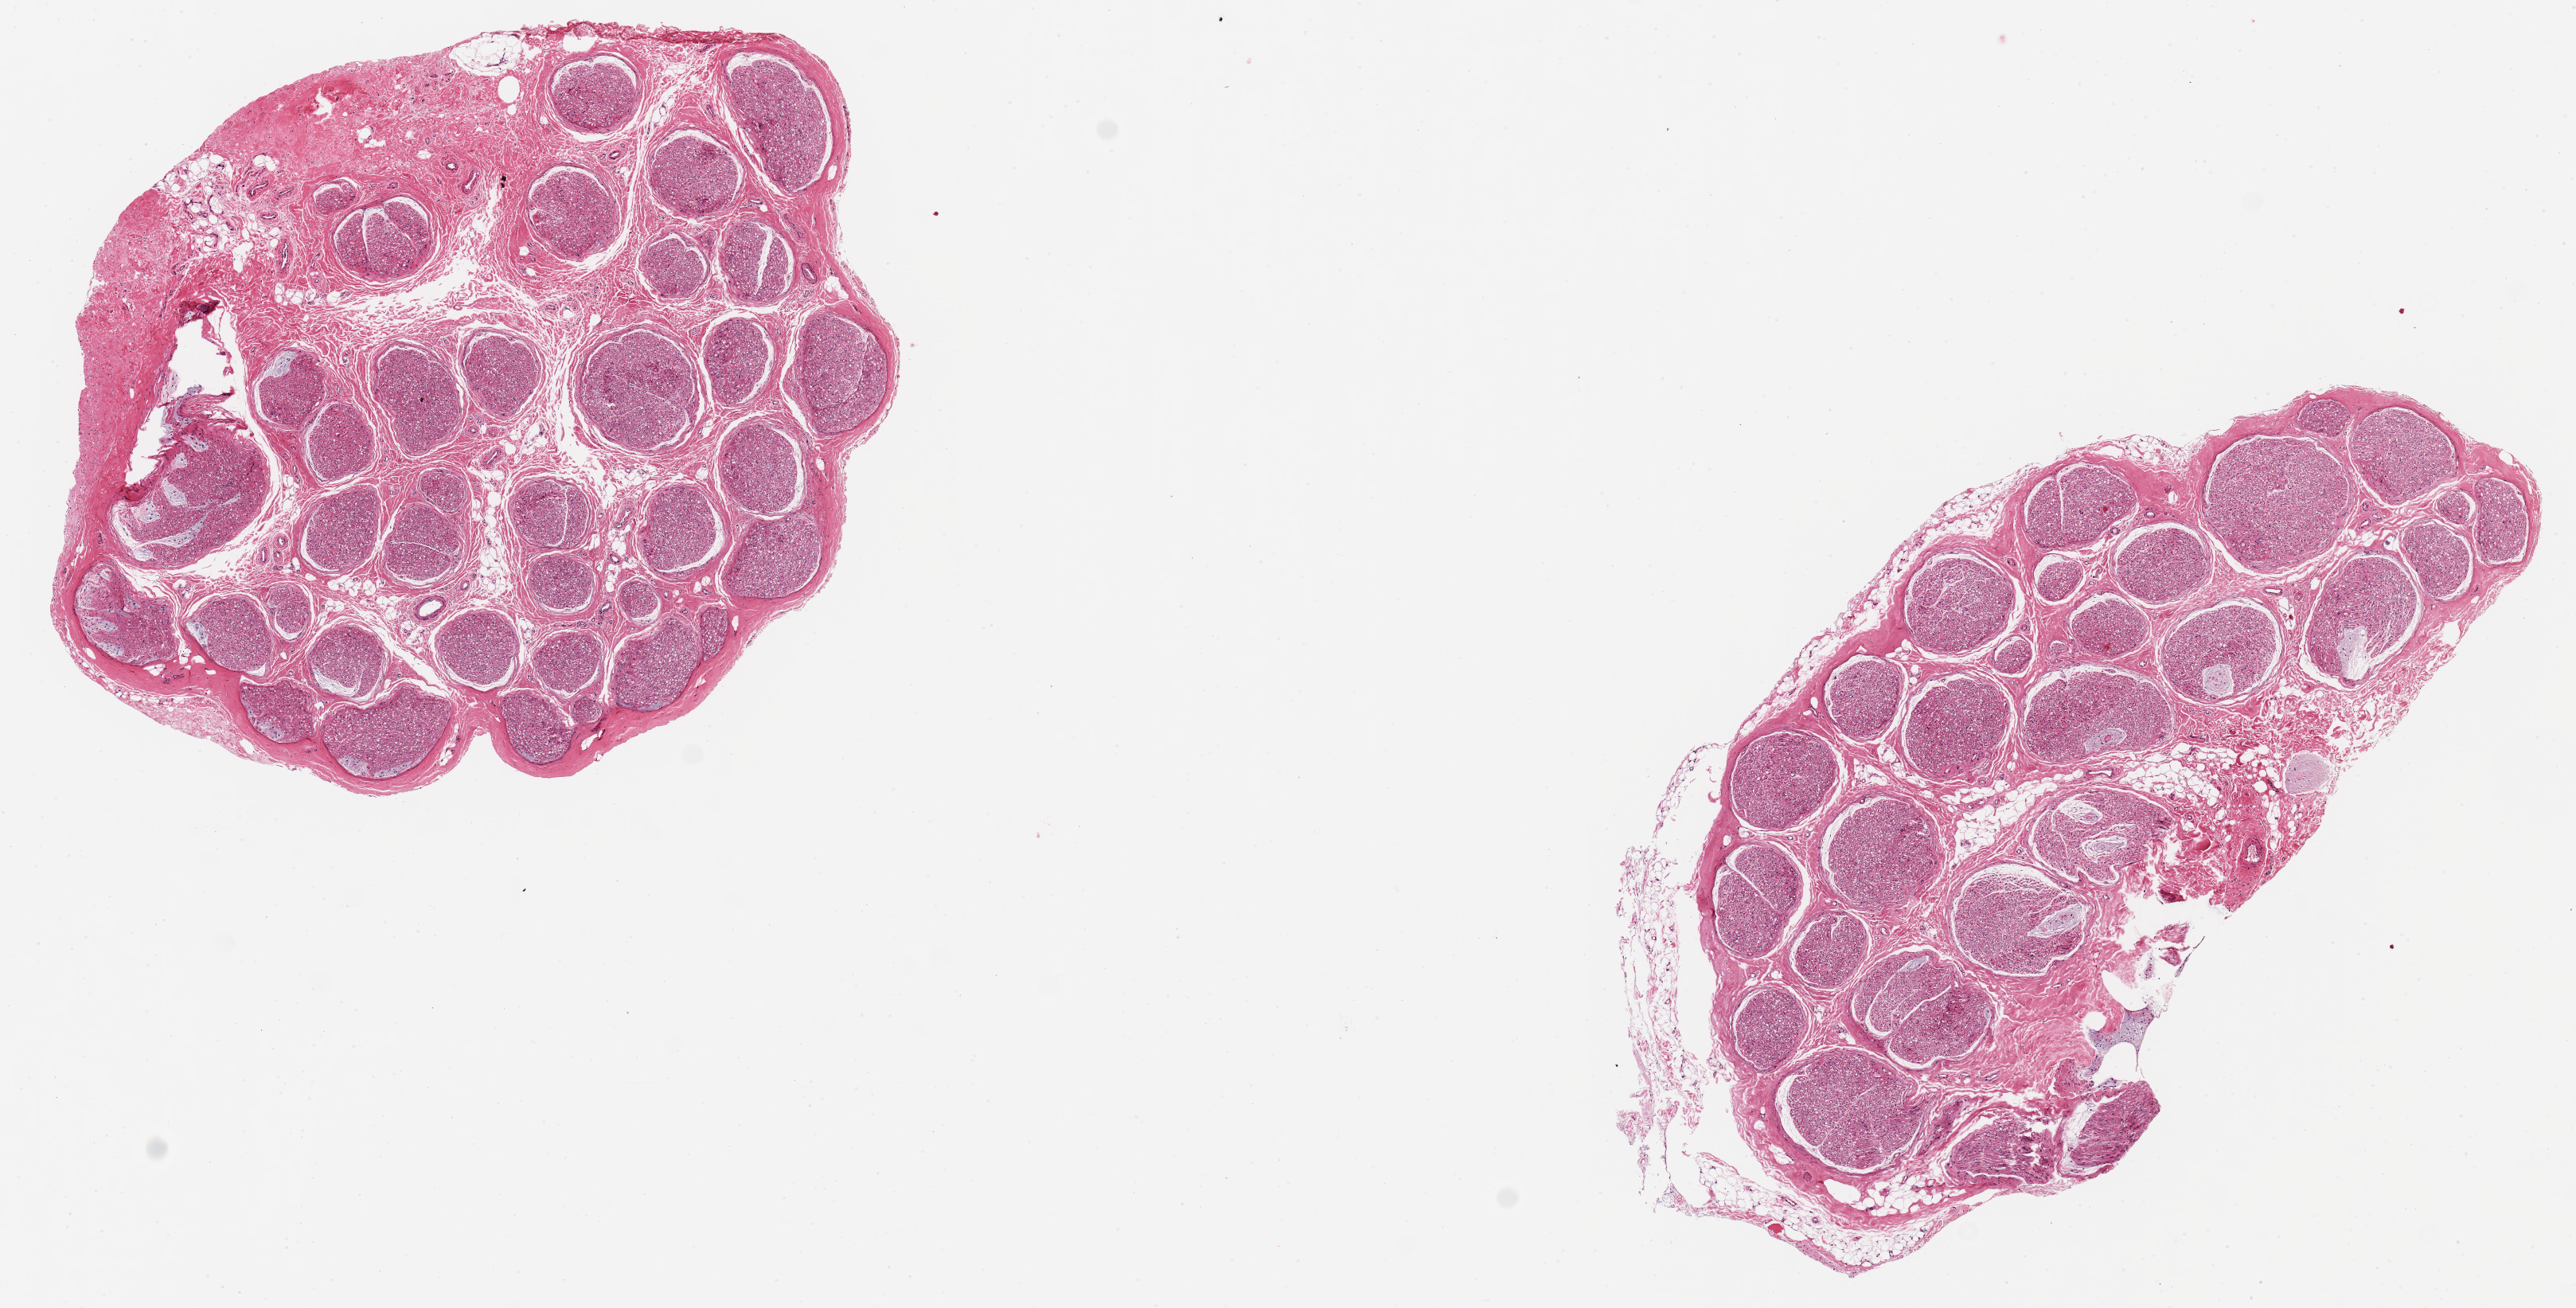
Whole-slide image, H&E stain, a low-resolution overview of the entire scanned area, about 12.8 x 6.5 mm (acquisition: 20x scan). PAXgene-fixed, paraffin-embedded tissue. Target tissue: tibial nerve. Donor tissue sample. Donor sex: female.
• reviewer comment on this tissue sample: 2 aliquots, ~4.5mm d . Good clean specimens